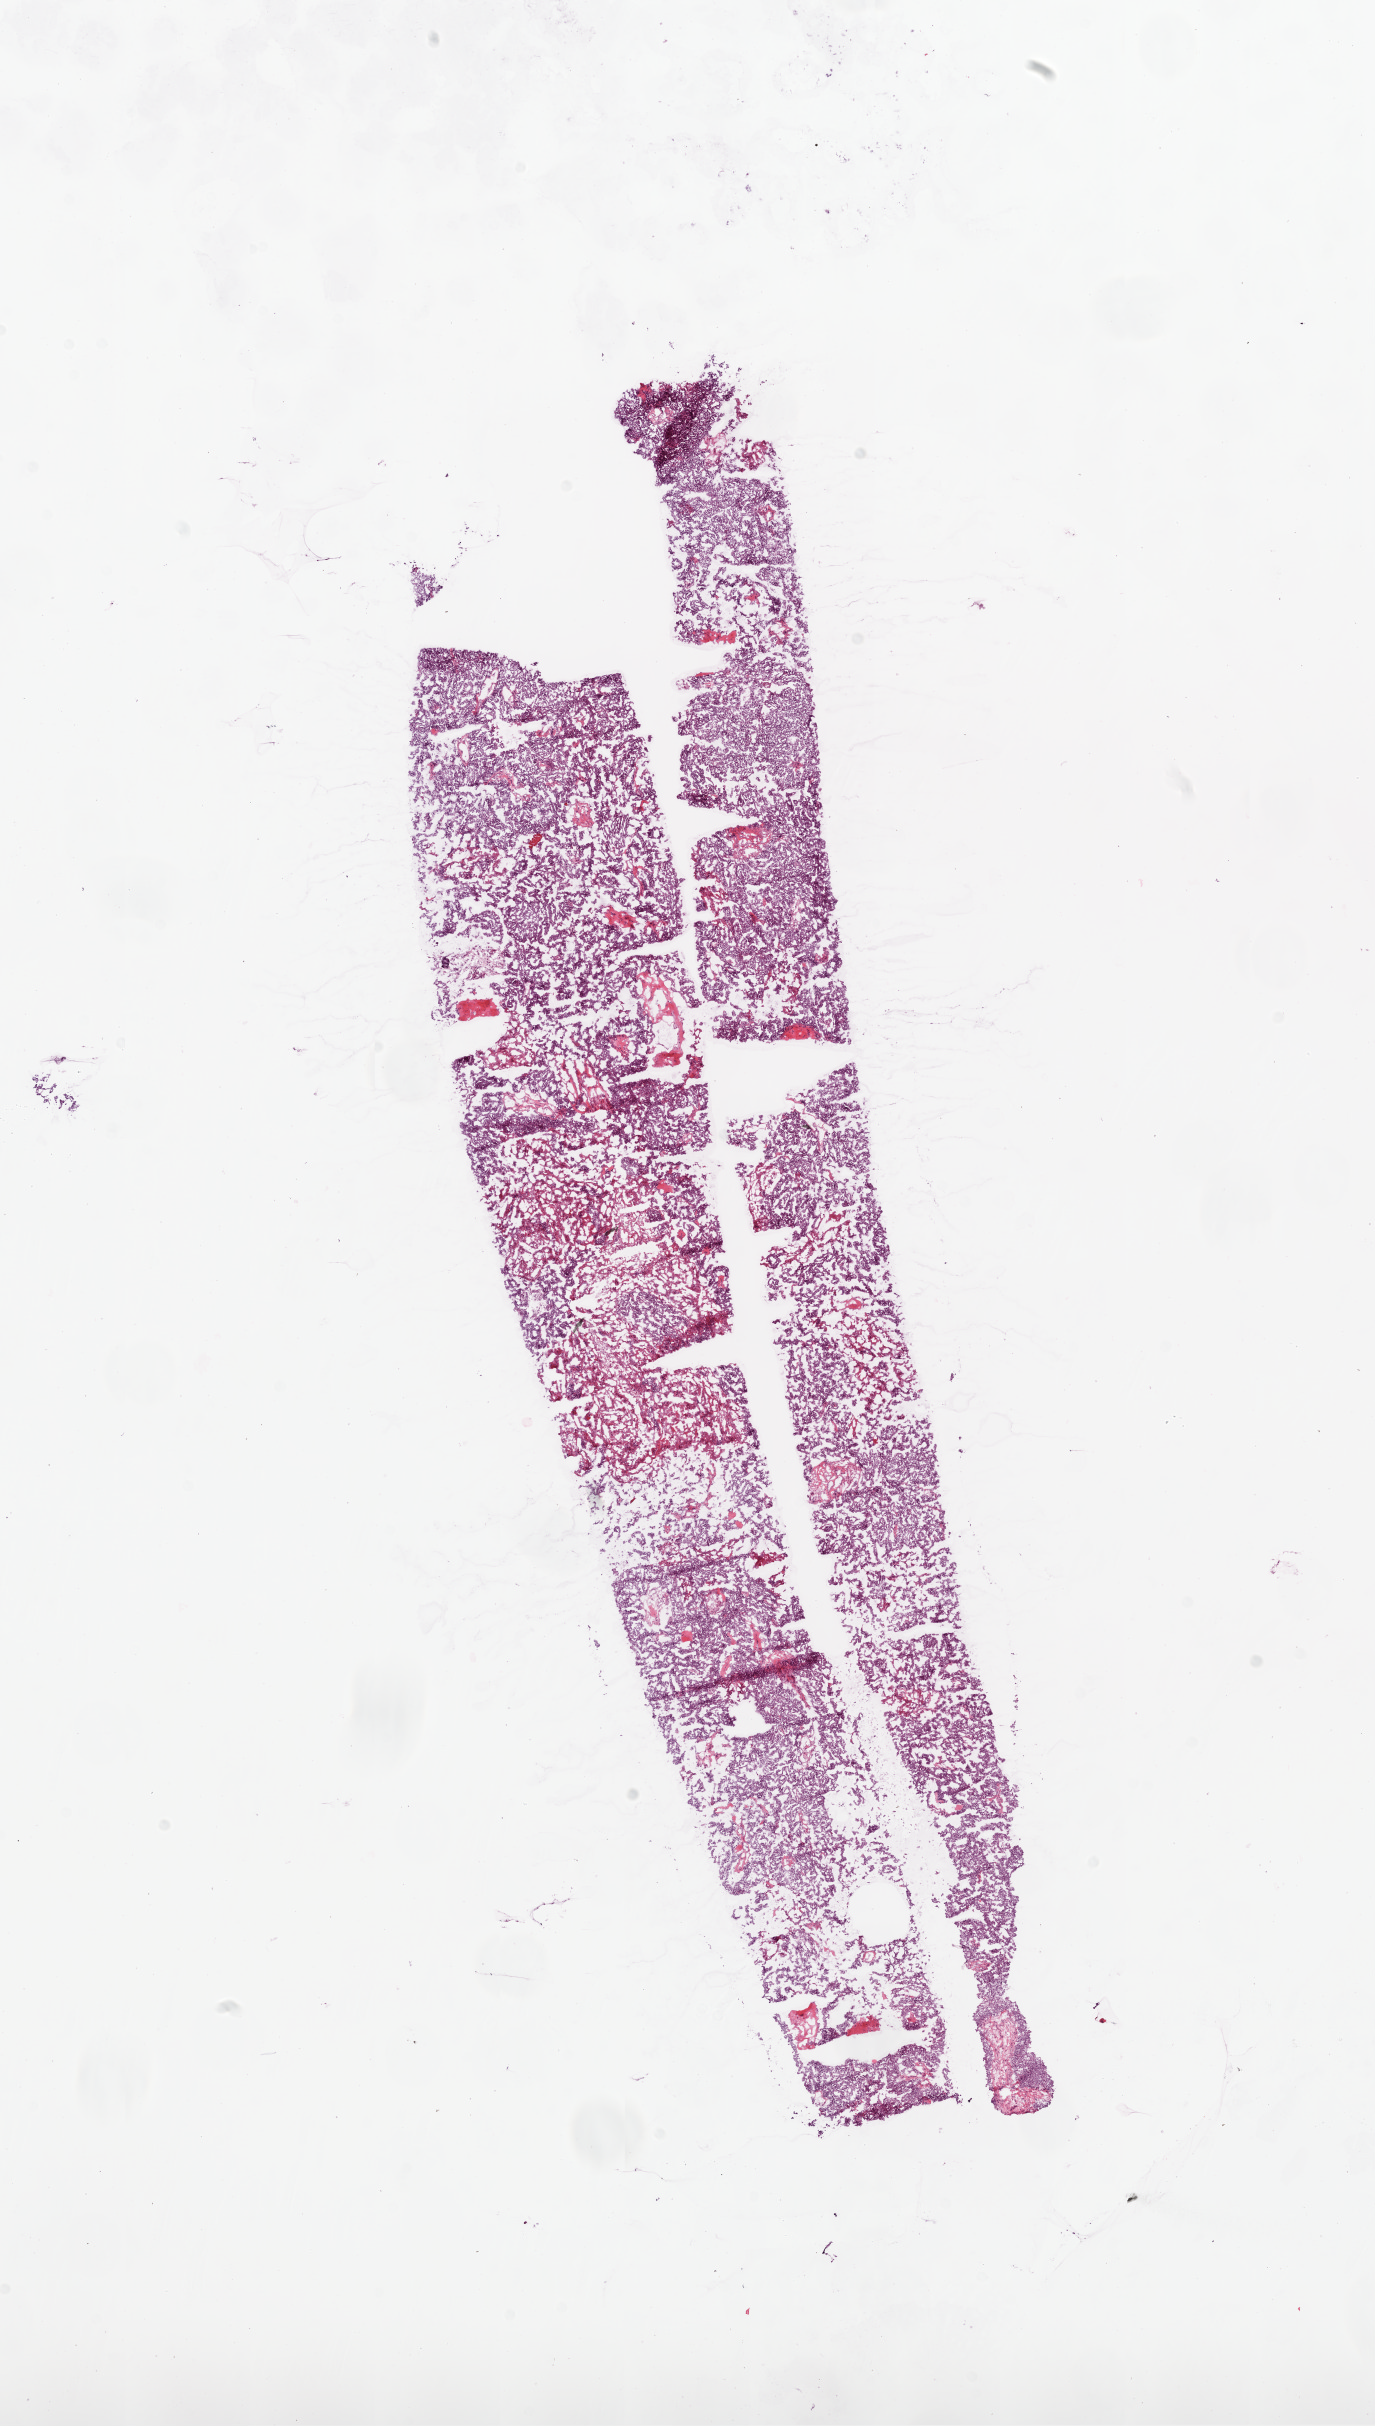
H&E-stained whole-slide image, shown as a low-resolution overview of the whole scanned area (about 11.0 x 19.5 mm, from a 20x scan). Frozen section from the bottom of the tissue portion. Primary tumour sample from the ovary. Female patient; age at initial diagnosis 57 years. Histologic grade: G3 (poorly differentiated). Slide review estimates, as recorded: tumour cells 90%, tumour nuclei 99%, normal cells 0%, stromal cells 5%, necrosis 5%.
FIGO stage: IV. Diagnosis: Serous cystadenocarcinoma, NOS.